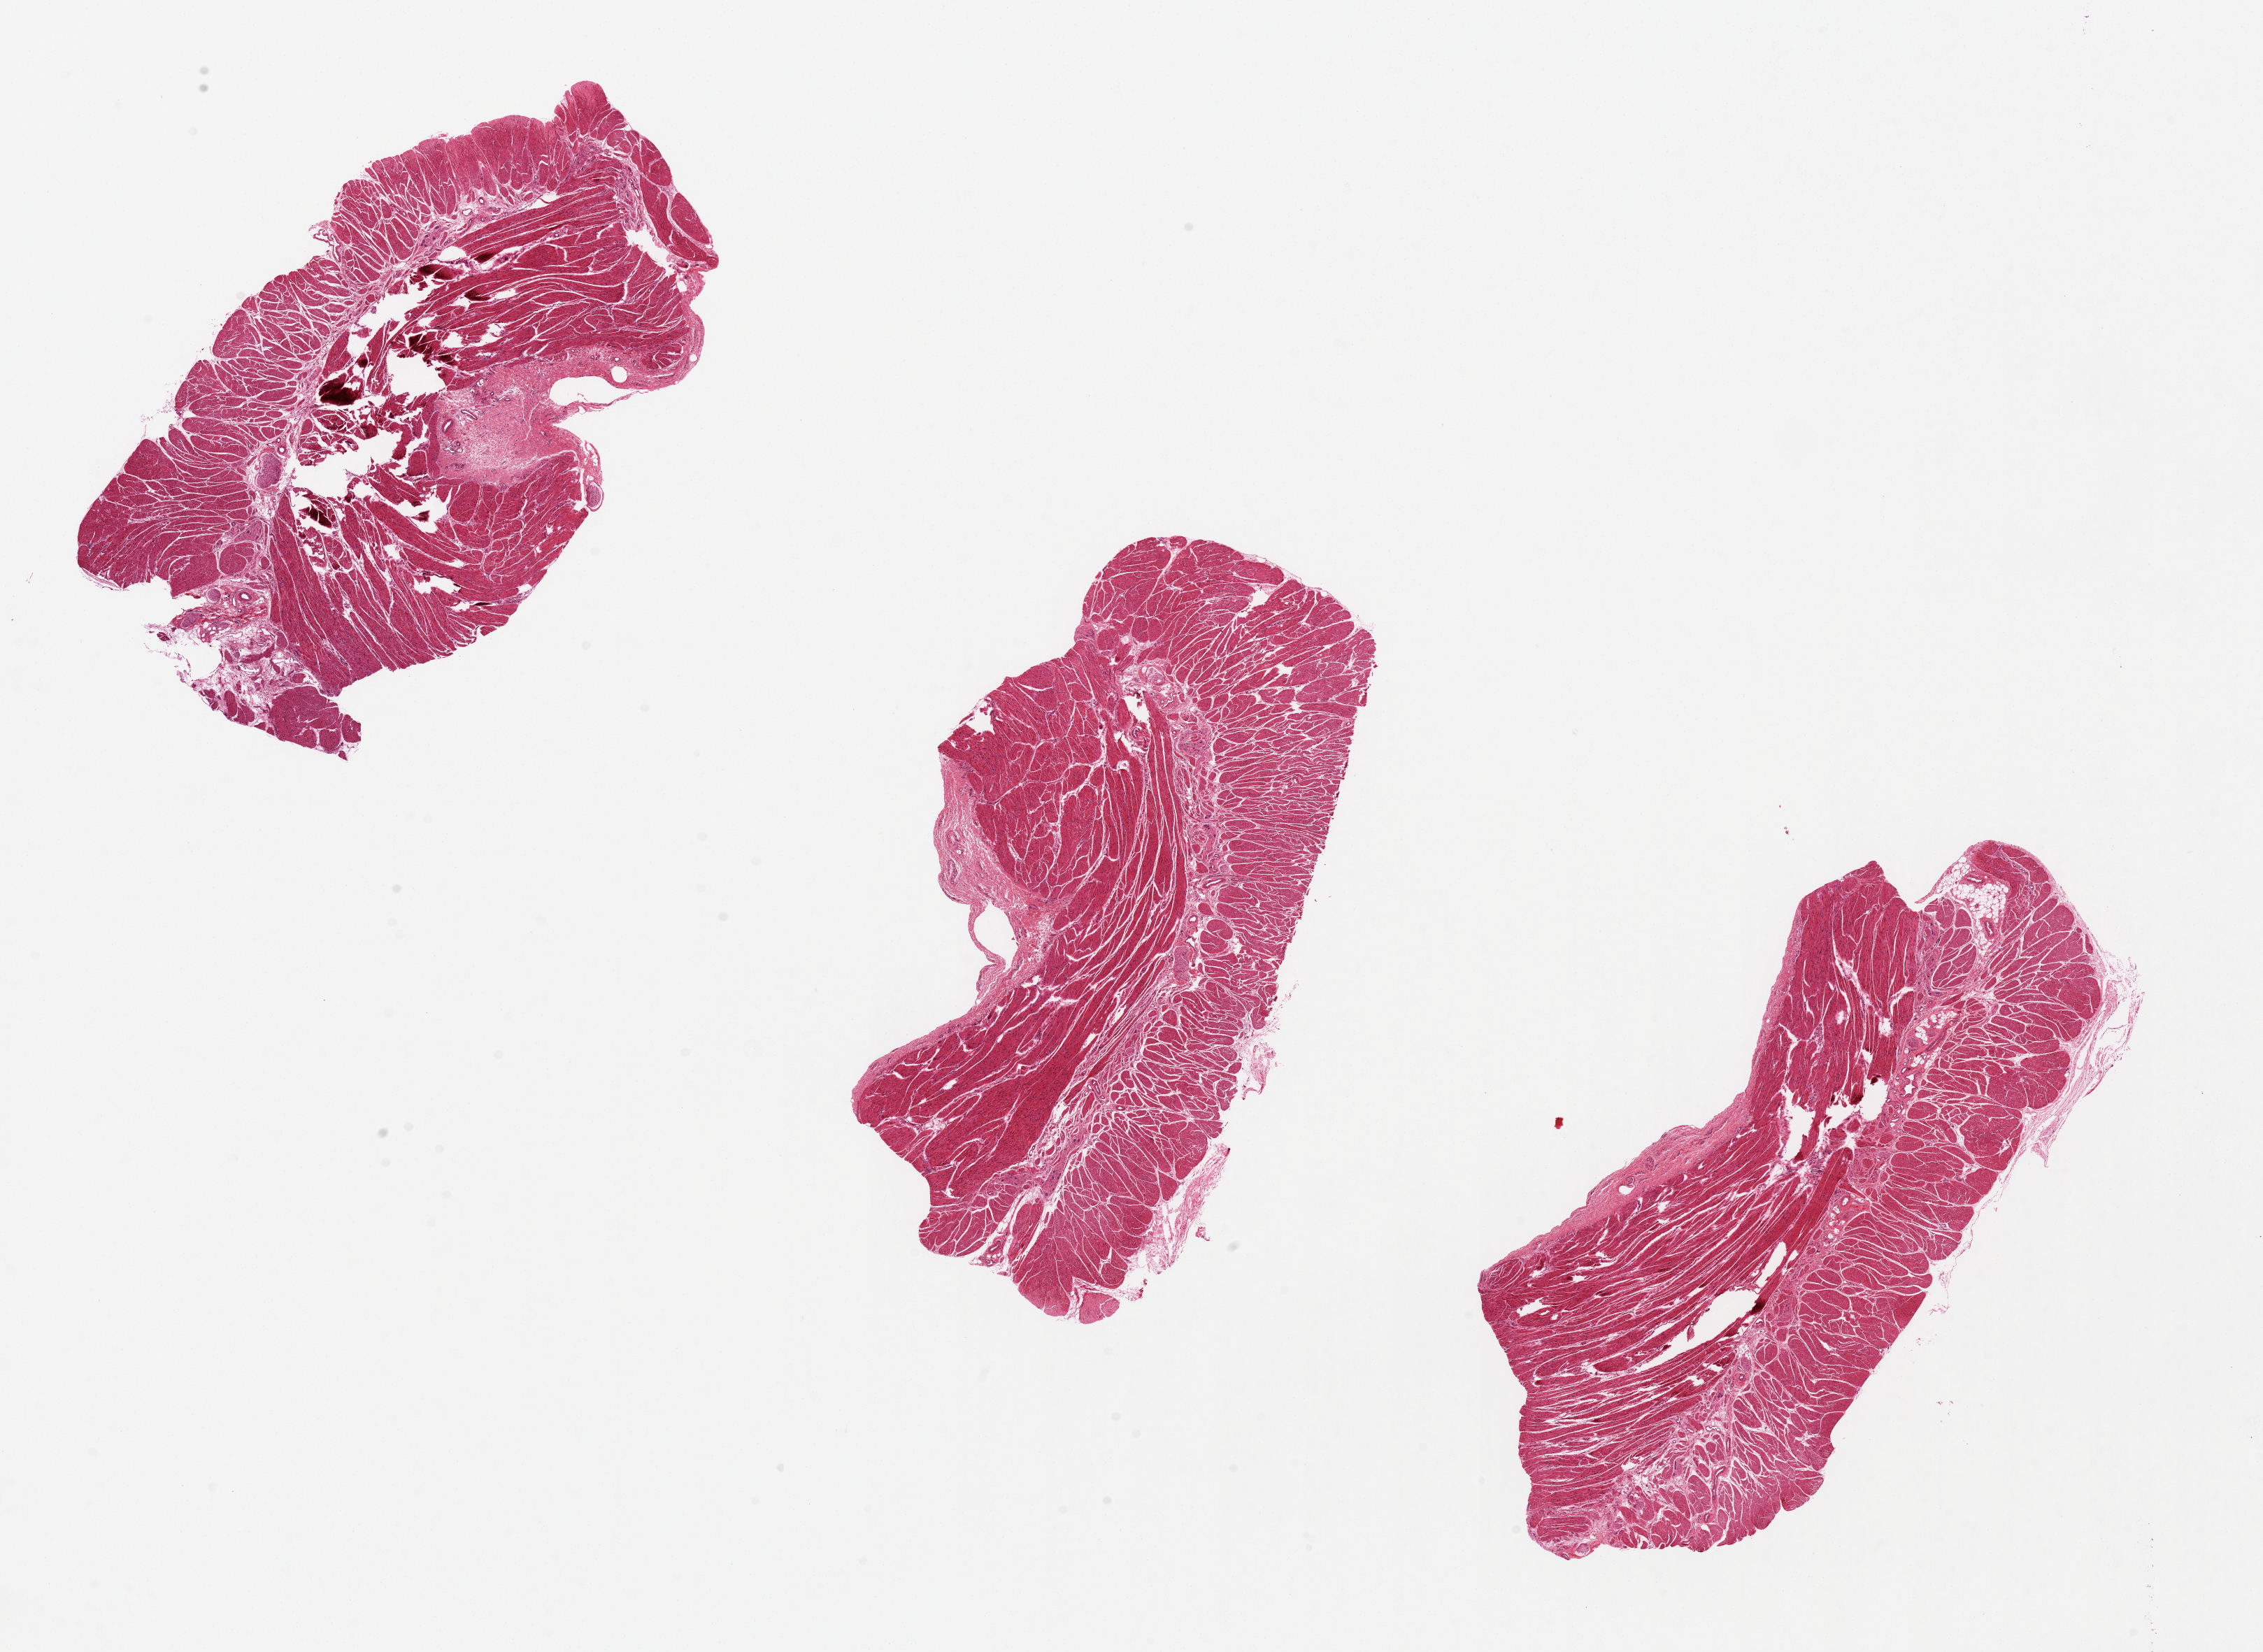
Digitized hematoxylin and eosin (H&E)-stained section — shown as a low-resolution overview of the whole scanned area (about 25.6 x 18.7 mm, acquisition: 20x scan); PAXgene-fixed, paraffin-embedded tissue; sampled site (target tissue): esophageal muscle; tissue donor sample.
* reviewer comment on this tissue sample: 0-1. One of three pieces with poor central fixation, sizes average 9x4mm